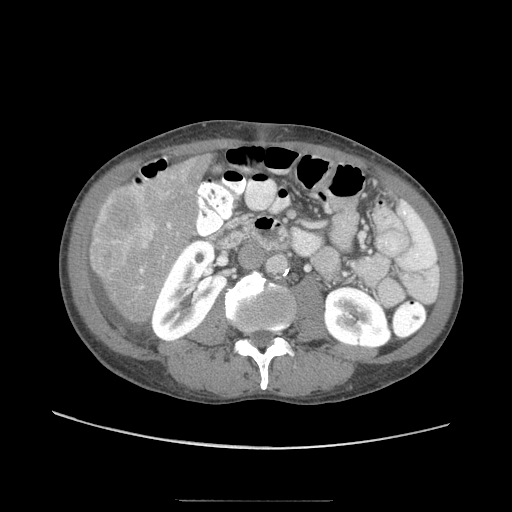
Contrast-enhanced abdominal CT (liver protocol), one axial slice. Slice 15 of 103 in the series (ordered by position). Reconstruction kernel STANDARD. Soft-tissue window (W 400 / L 40 HU). 2.5 mm slice thickness. 512 × 512 image matrix, field of view 380 × 380 mm. From the clinical record (not read from this slice): diagnosis: hepatocellular carcinoma (patient treated with transarterial chemoembolisation; whether this scan precedes or follows treatment is not stated here); TNM stage (as recorded): Stage-IIIA; Child-Pugh class: A; tumour differentiation: moderately differentiated; tumour size: 16 cm.
Structures marked on this image (semi-automatic segmentation, software-assisted and operator-edited):
- liver parenchyma outside the tumour (the mass and vessels are separate outlines, so this box may not span the whole liver): bounding box <88,152,212,324> (left, top, right, bottom; pixels)
- mass: <90,182,159,275>